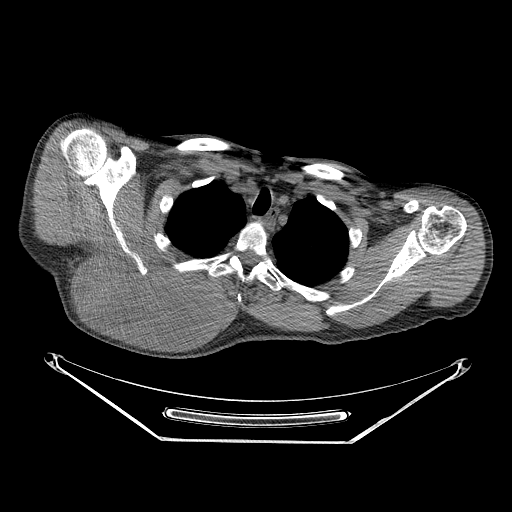
CT of an extremity soft-tissue mass (from a PET/CT study), one axial slice; position 198 of 267 along the scan axis; reconstruction kernel STANDARD; 140 kVp; soft-tissue window (W 400 / L 40 HU); 512 × 512 image matrix, field of view 500 × 500 mm. Male patient. From the clinical record (not read from this slice): histological type: pleiomorphic spindle cell undifferentiated; grade: high; site of the primary tumour: right parascapusular.
Annotated regions visible in this slice (expert contour drawn on MRI and transferred to this co-registered scan by the dataset authors):
- gross tumour volume including surrounding oedema: box from (x=75, y=253) to (x=234, y=337) px
- gross tumour volume (mass): (x=77, y=254)–(x=220, y=334)